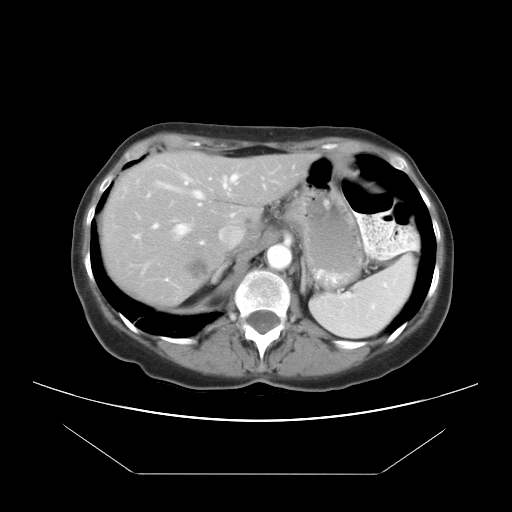
Contrast-enhanced abdominal CT, one axial slice. Position 16 of 21 along the scan axis. Reconstruction kernel STANDARD. Intravenous contrast given. Soft-tissue window (W 400 / L 40 HU). 7.5 mm slice thickness. 512 × 512 image matrix, field of view 392 × 392 mm. Female patient, age 72 years. Case-level facts recorded for this patient, not image findings: diagnosis: colorectal cancer liver metastases, imaged before liver resection; multiple liver metastases: yes; largest metastasis: 4 cm; chemotherapy before resection: yes.
Structures marked on this image (manually delineated by an expert):
- hepatic veins: box from (x=158, y=174) to (x=238, y=238) px
- liver: (x=103, y=154)–(x=306, y=306)
- planned liver remnant (the part of the liver to remain after resection): (x=103, y=154)–(x=305, y=276)
- portal vein (with intrahepatic branches): (x=153, y=204)–(x=200, y=229)
- liver metastasis: (x=242, y=216)–(x=255, y=227)
- liver metastasis: (x=212, y=171)–(x=222, y=179)
- liver metastasis: (x=184, y=257)–(x=210, y=281)